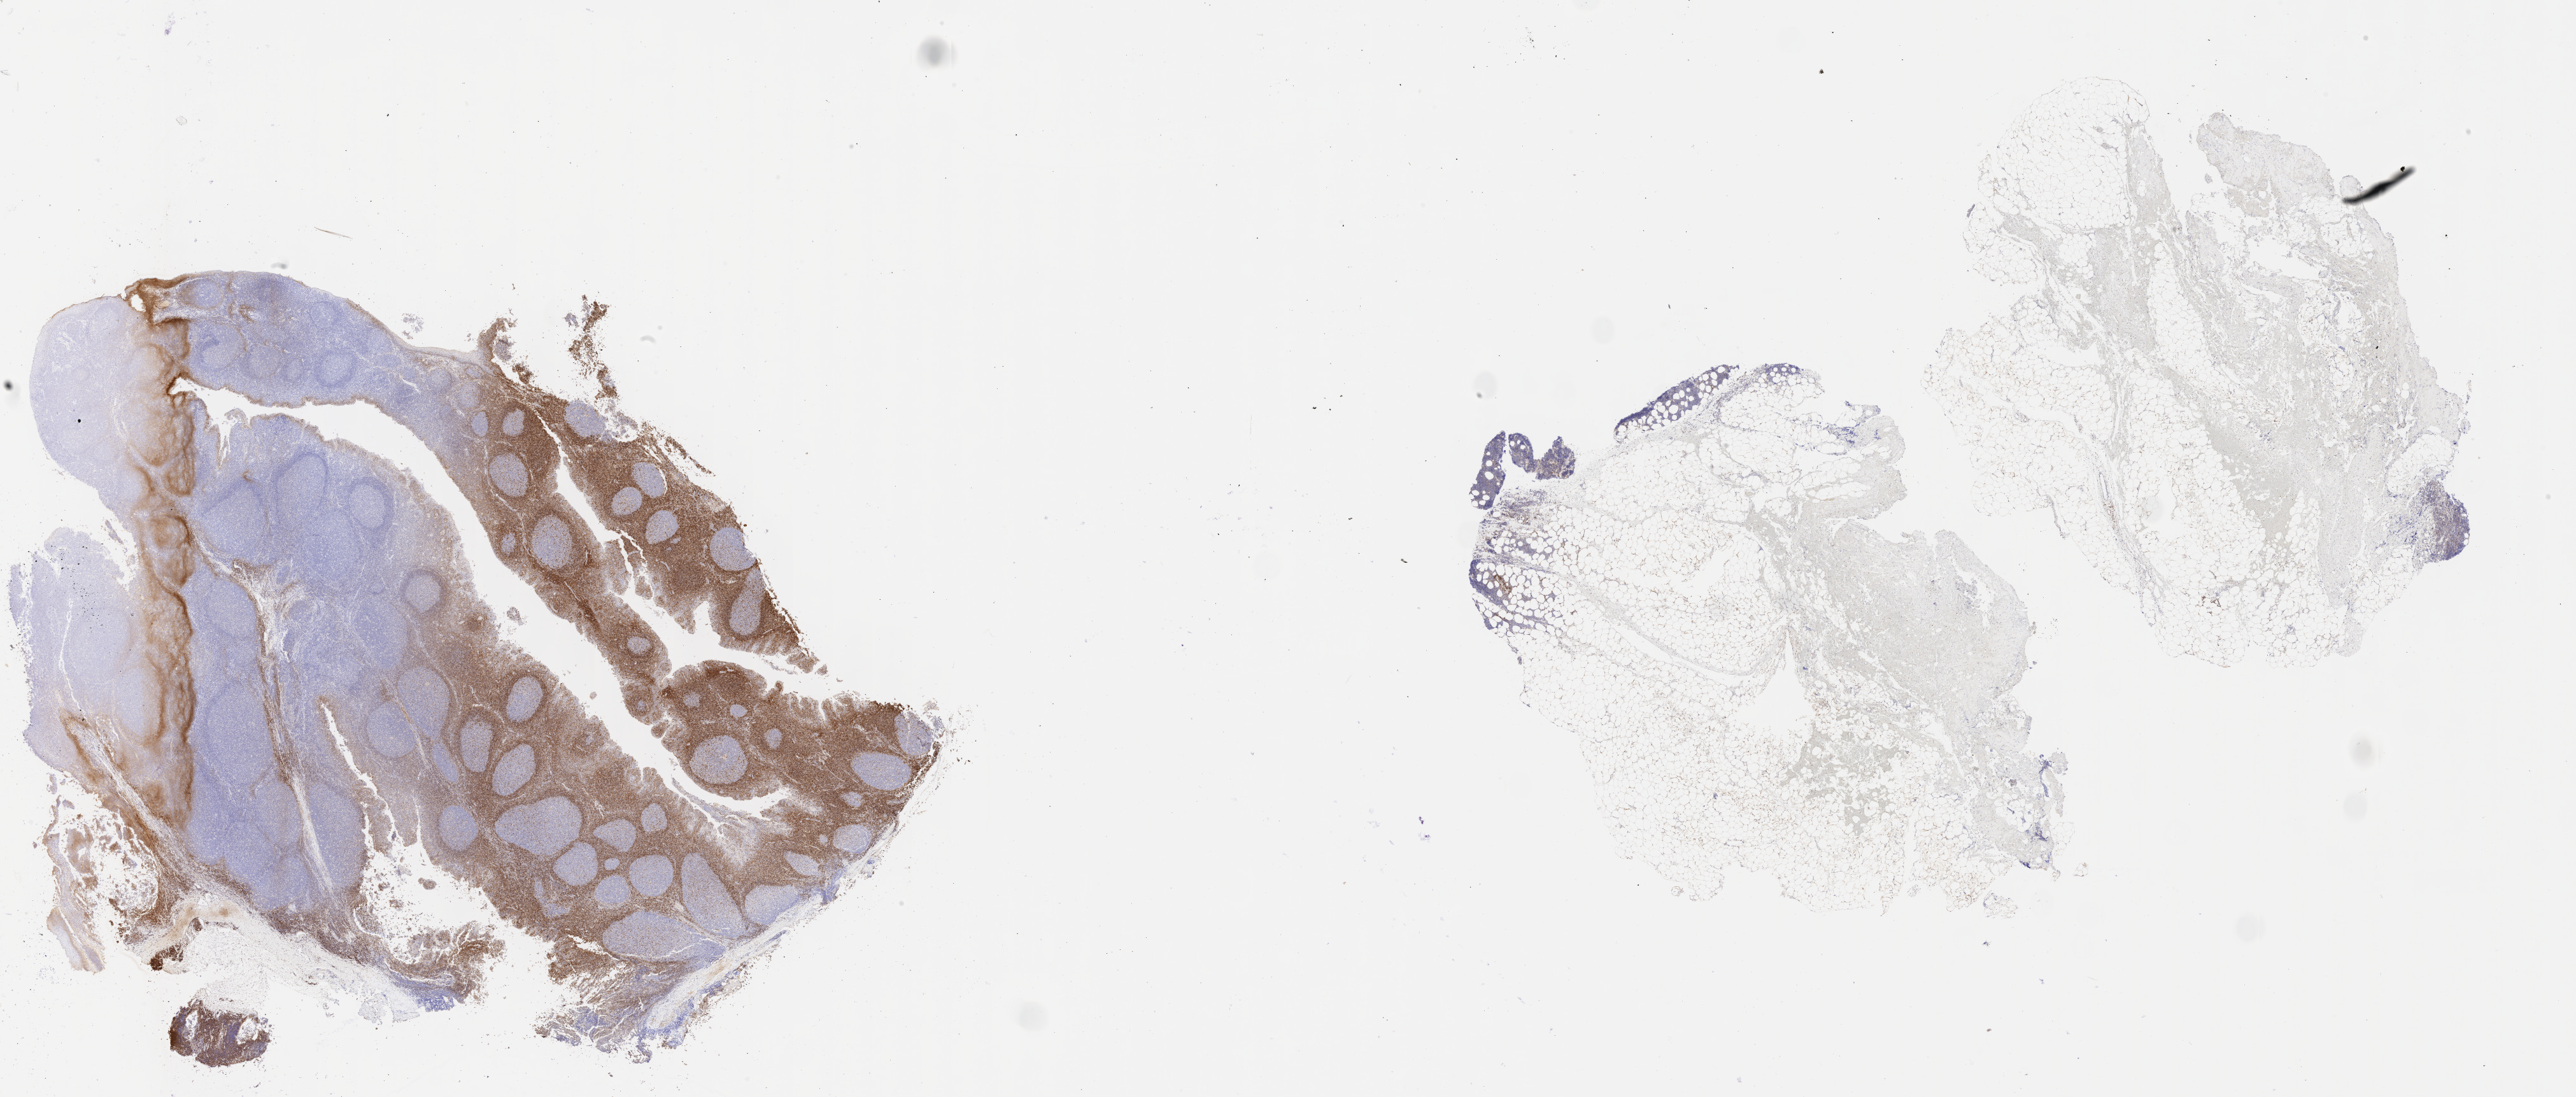
IHC for BCL2, whole-slide image — shown as a low-resolution overview of the whole scanned area (about 32.7 x 13.9 mm). Tumor tissue. Site: upper limb lymph node. Patient: male, age 76 years.
Histologic diagnosis: Burkitt lymphoma, NOS.